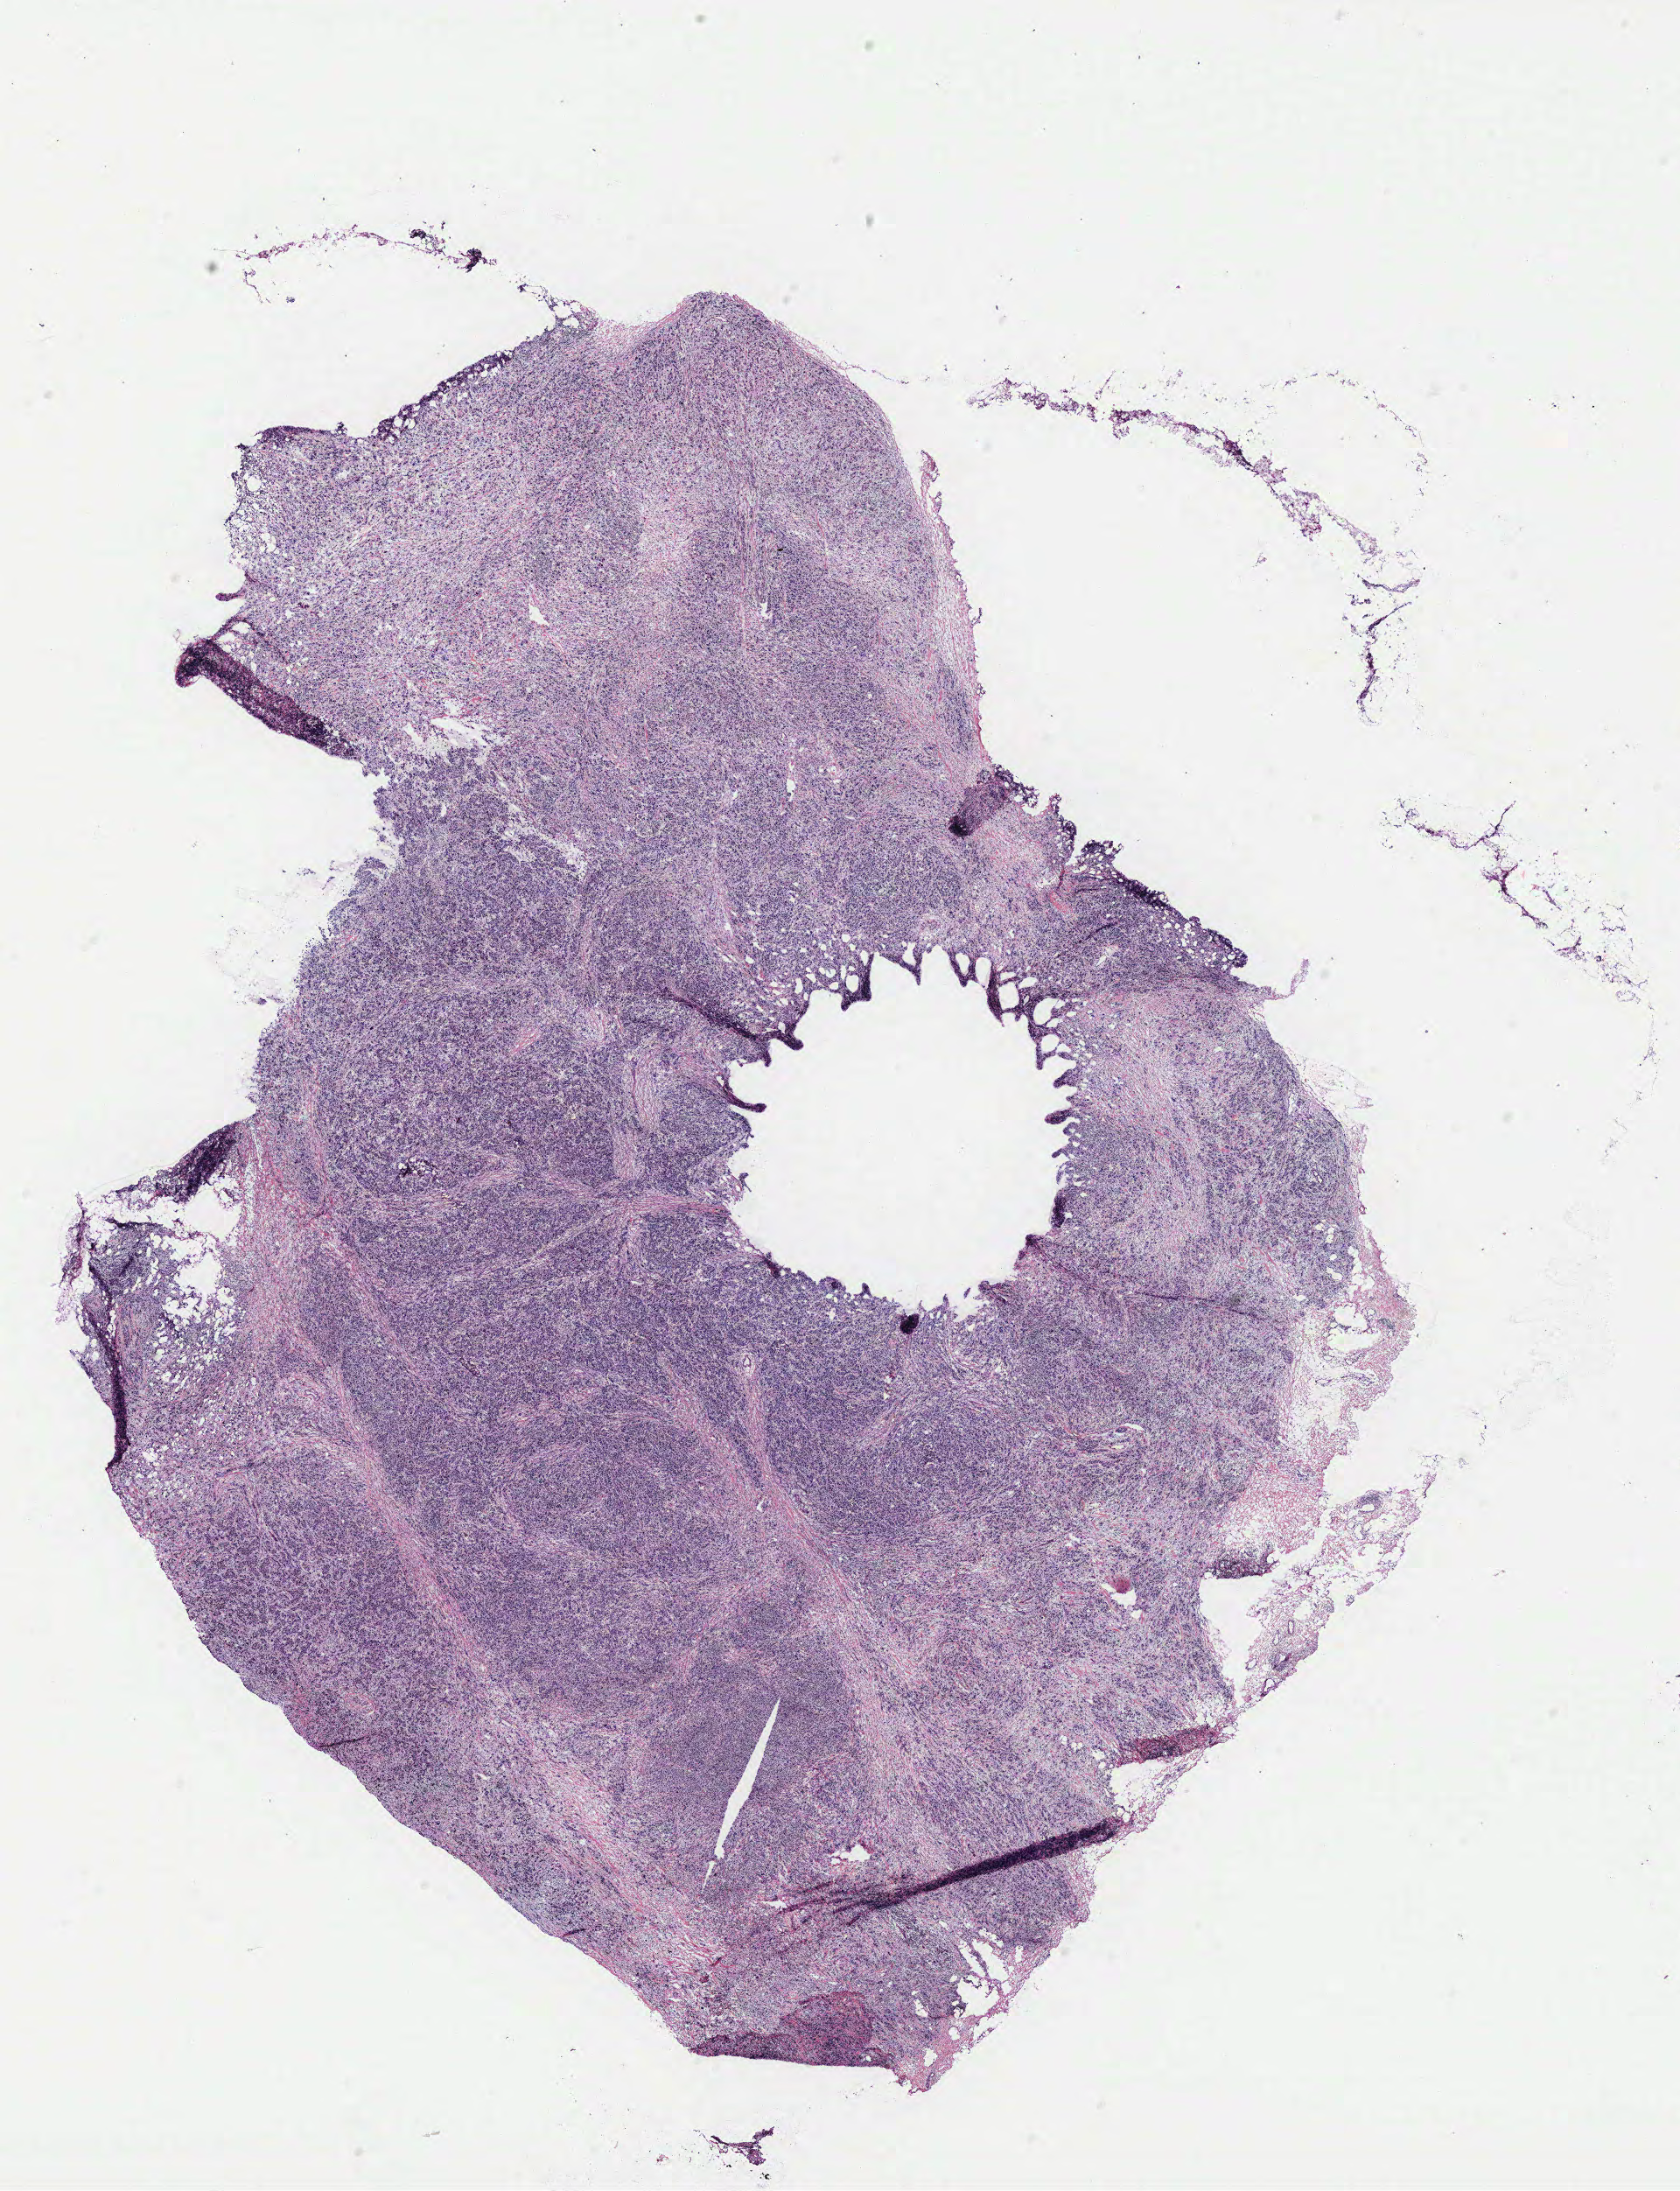
H&E whole-slide image — a low-resolution overview of the entire scanned area, about 15.4 x 20.0 mm. Breast, tissue type not recorded. Female, 58 y/o.
- patient diagnosis: Infiltrating duct carcinoma, NOS